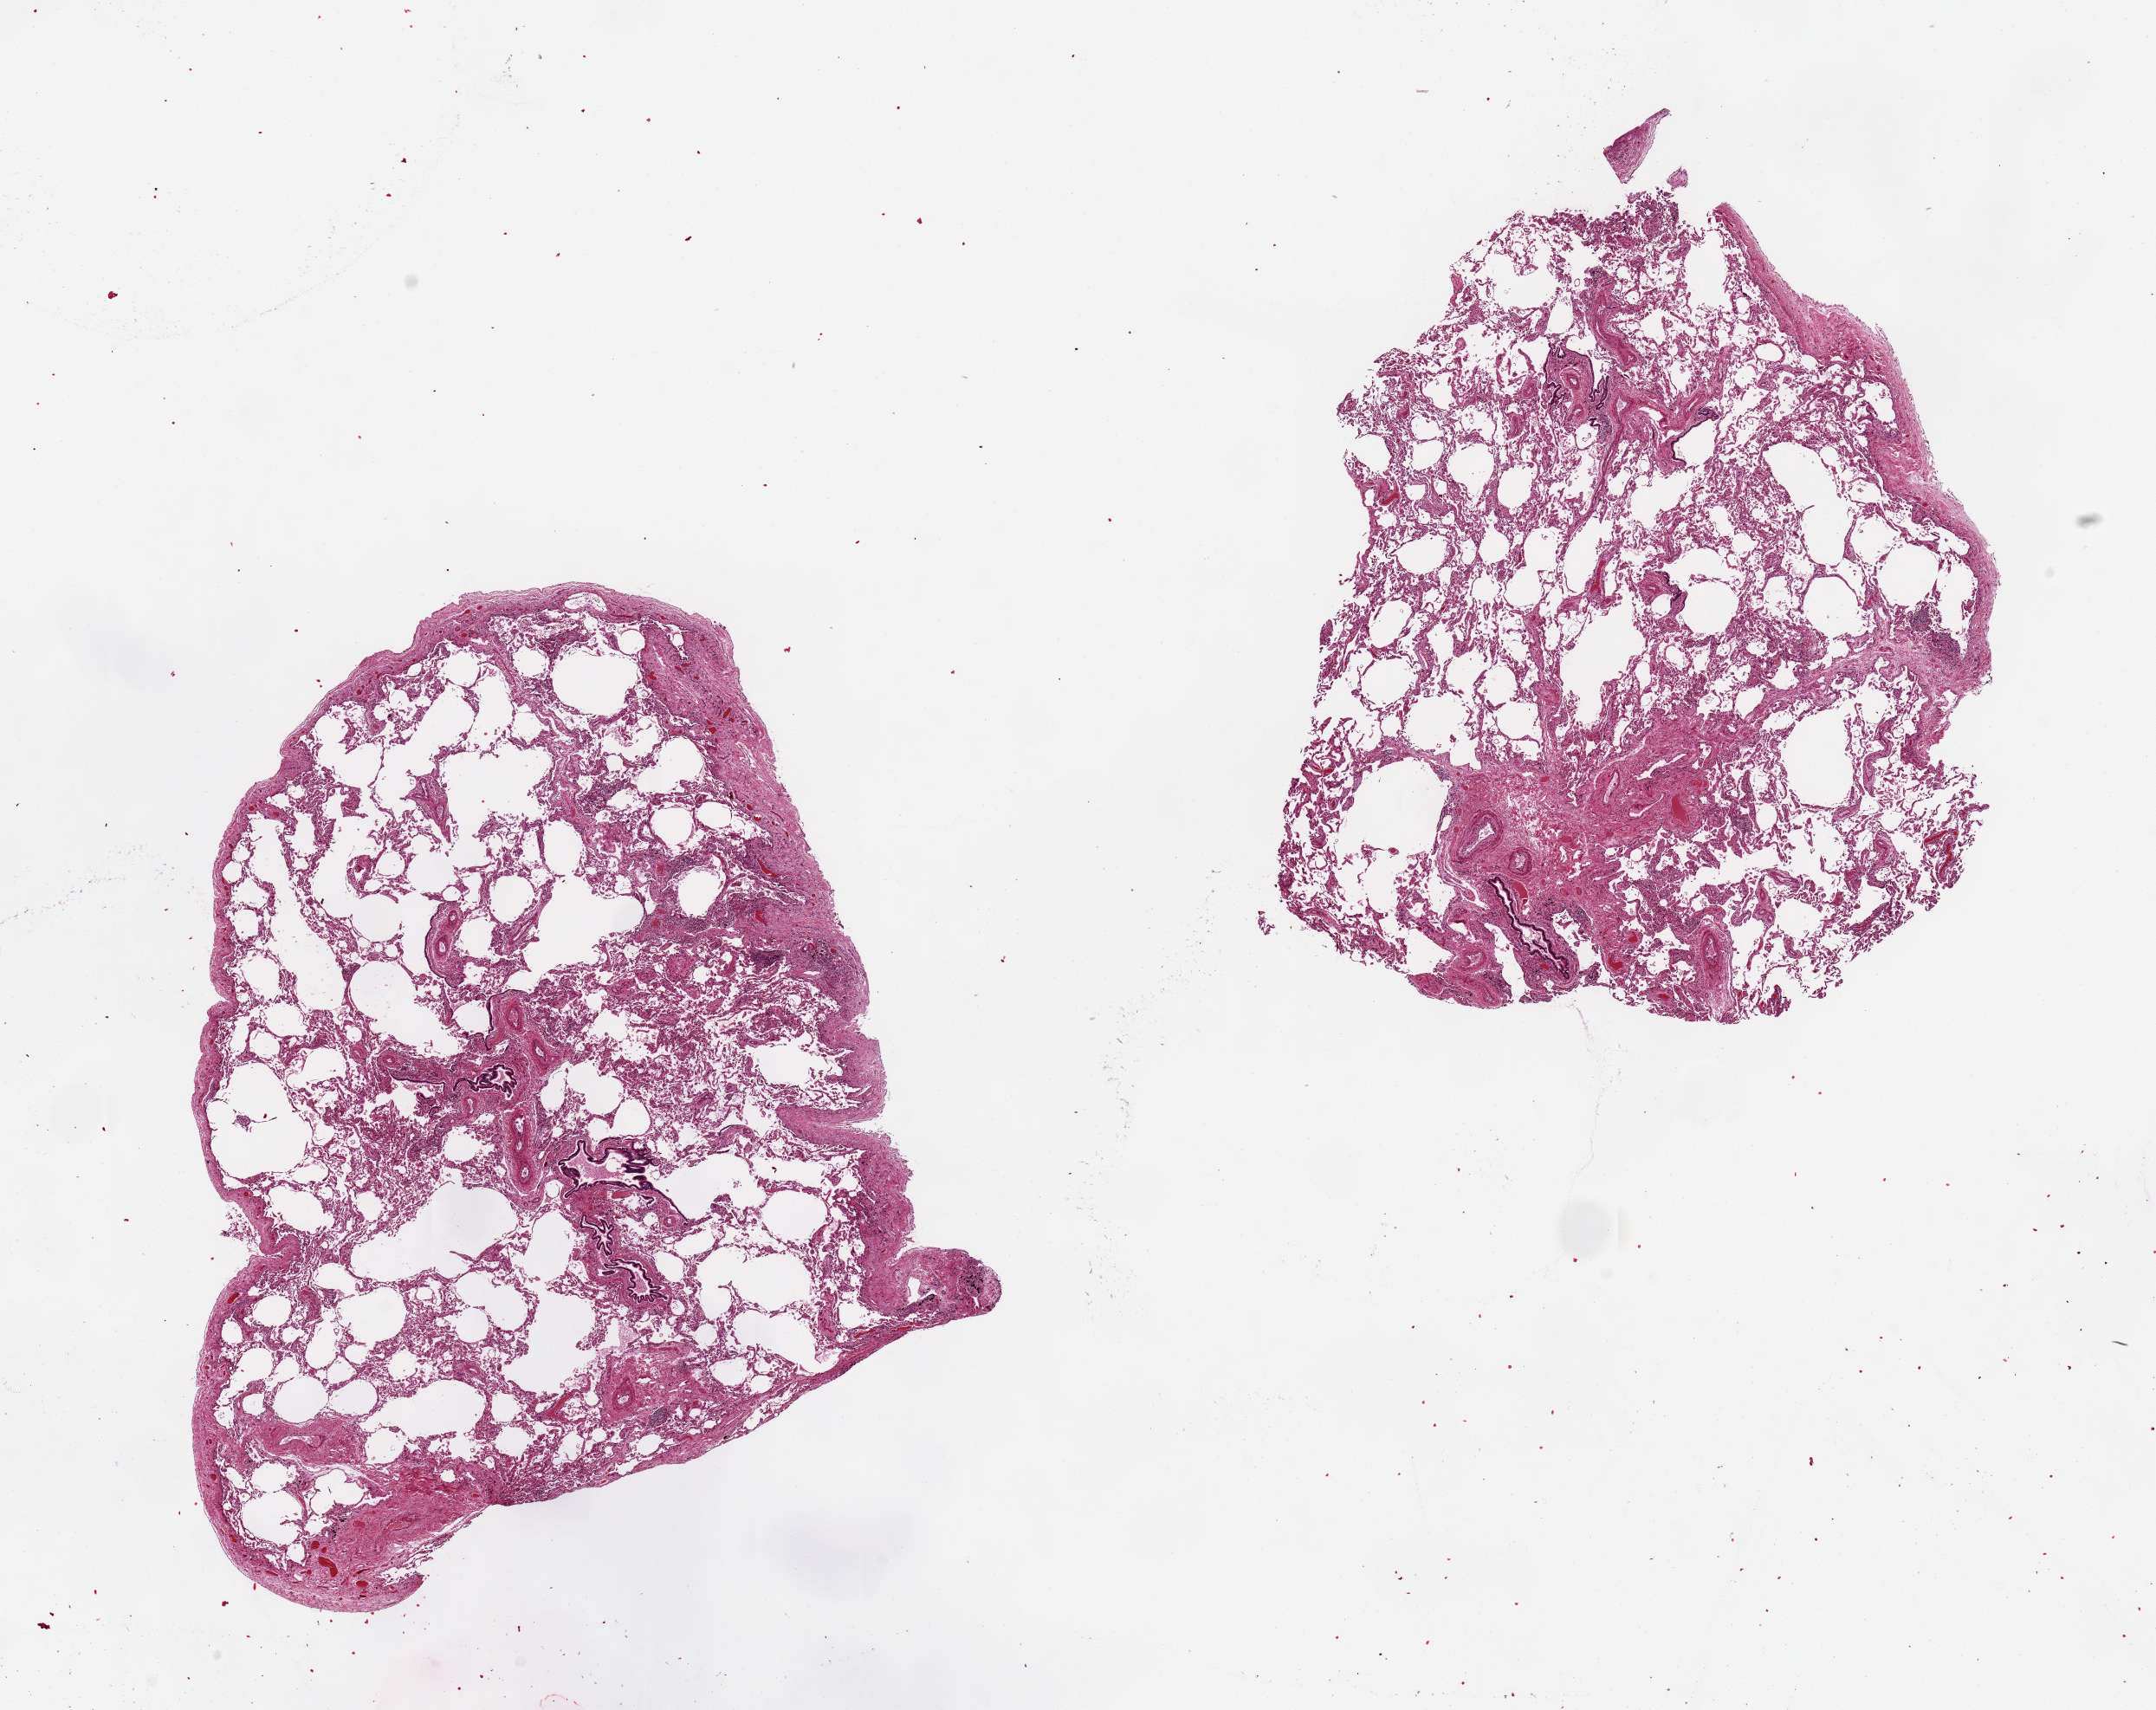
Digitized hematoxylin and eosin (H&E)-stained section — whole scanned area (about 19.7 x 15.6 mm) shown as a low-resolution overview, PAXgene-fixed paraffin-embedded (PFPE) section, target tissue: lung, tissue donor sample. Male donor.
Pathologist's review note for this sample: 2 pieces, 8x7 & 8x7.5mm; emphysema.